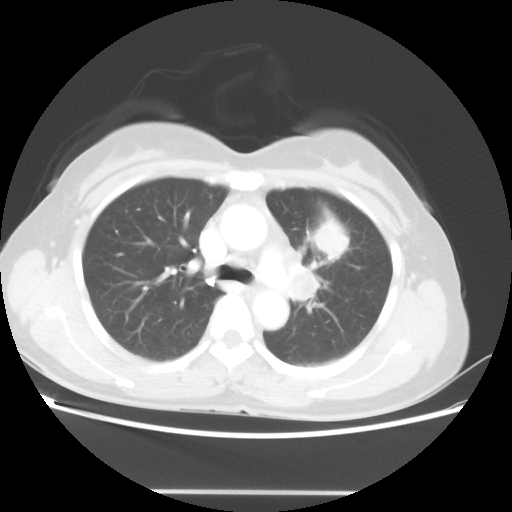
Chest CT, one axial slice. Slice 30 of 46 in the series (ordered by position). 100 kVp. Lung window (W 1500 / L -600 HU). 512 × 512 image matrix. Patient: female, 50 years. From the clinical record (not read from this slice): clinical TNM (as recorded): T1c N1 M0.
Outlined on this slice (bounding box drawn by a radiologist):
- lung tumour (recorded histology: adenocarcinoma): bounding box [x1, y1, x2, y2] px = [312, 219, 349, 261]